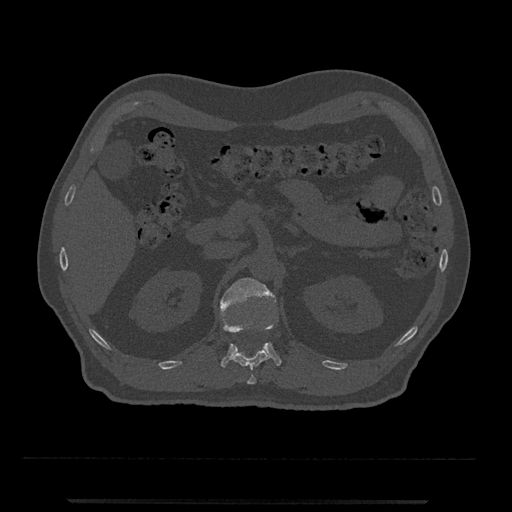
CT including the spine, one axial slice. Slice 369 of 797 in the series (ordered by position). Bone window (W 1800 / L 400 HU). 0.5 mm slice thickness. 512 × 512 image matrix. Male patient, age 63 years. Case-level facts recorded for this patient, not image findings: primary cancer: prostate.
Annotated regions visible in this slice (semi-automatically segmented with operator editing):
- L1 vertebra: bounding box [x1, y1, x2, y2] px = [220, 278, 281, 368]
- T12 vertebra: [231, 325, 270, 385]